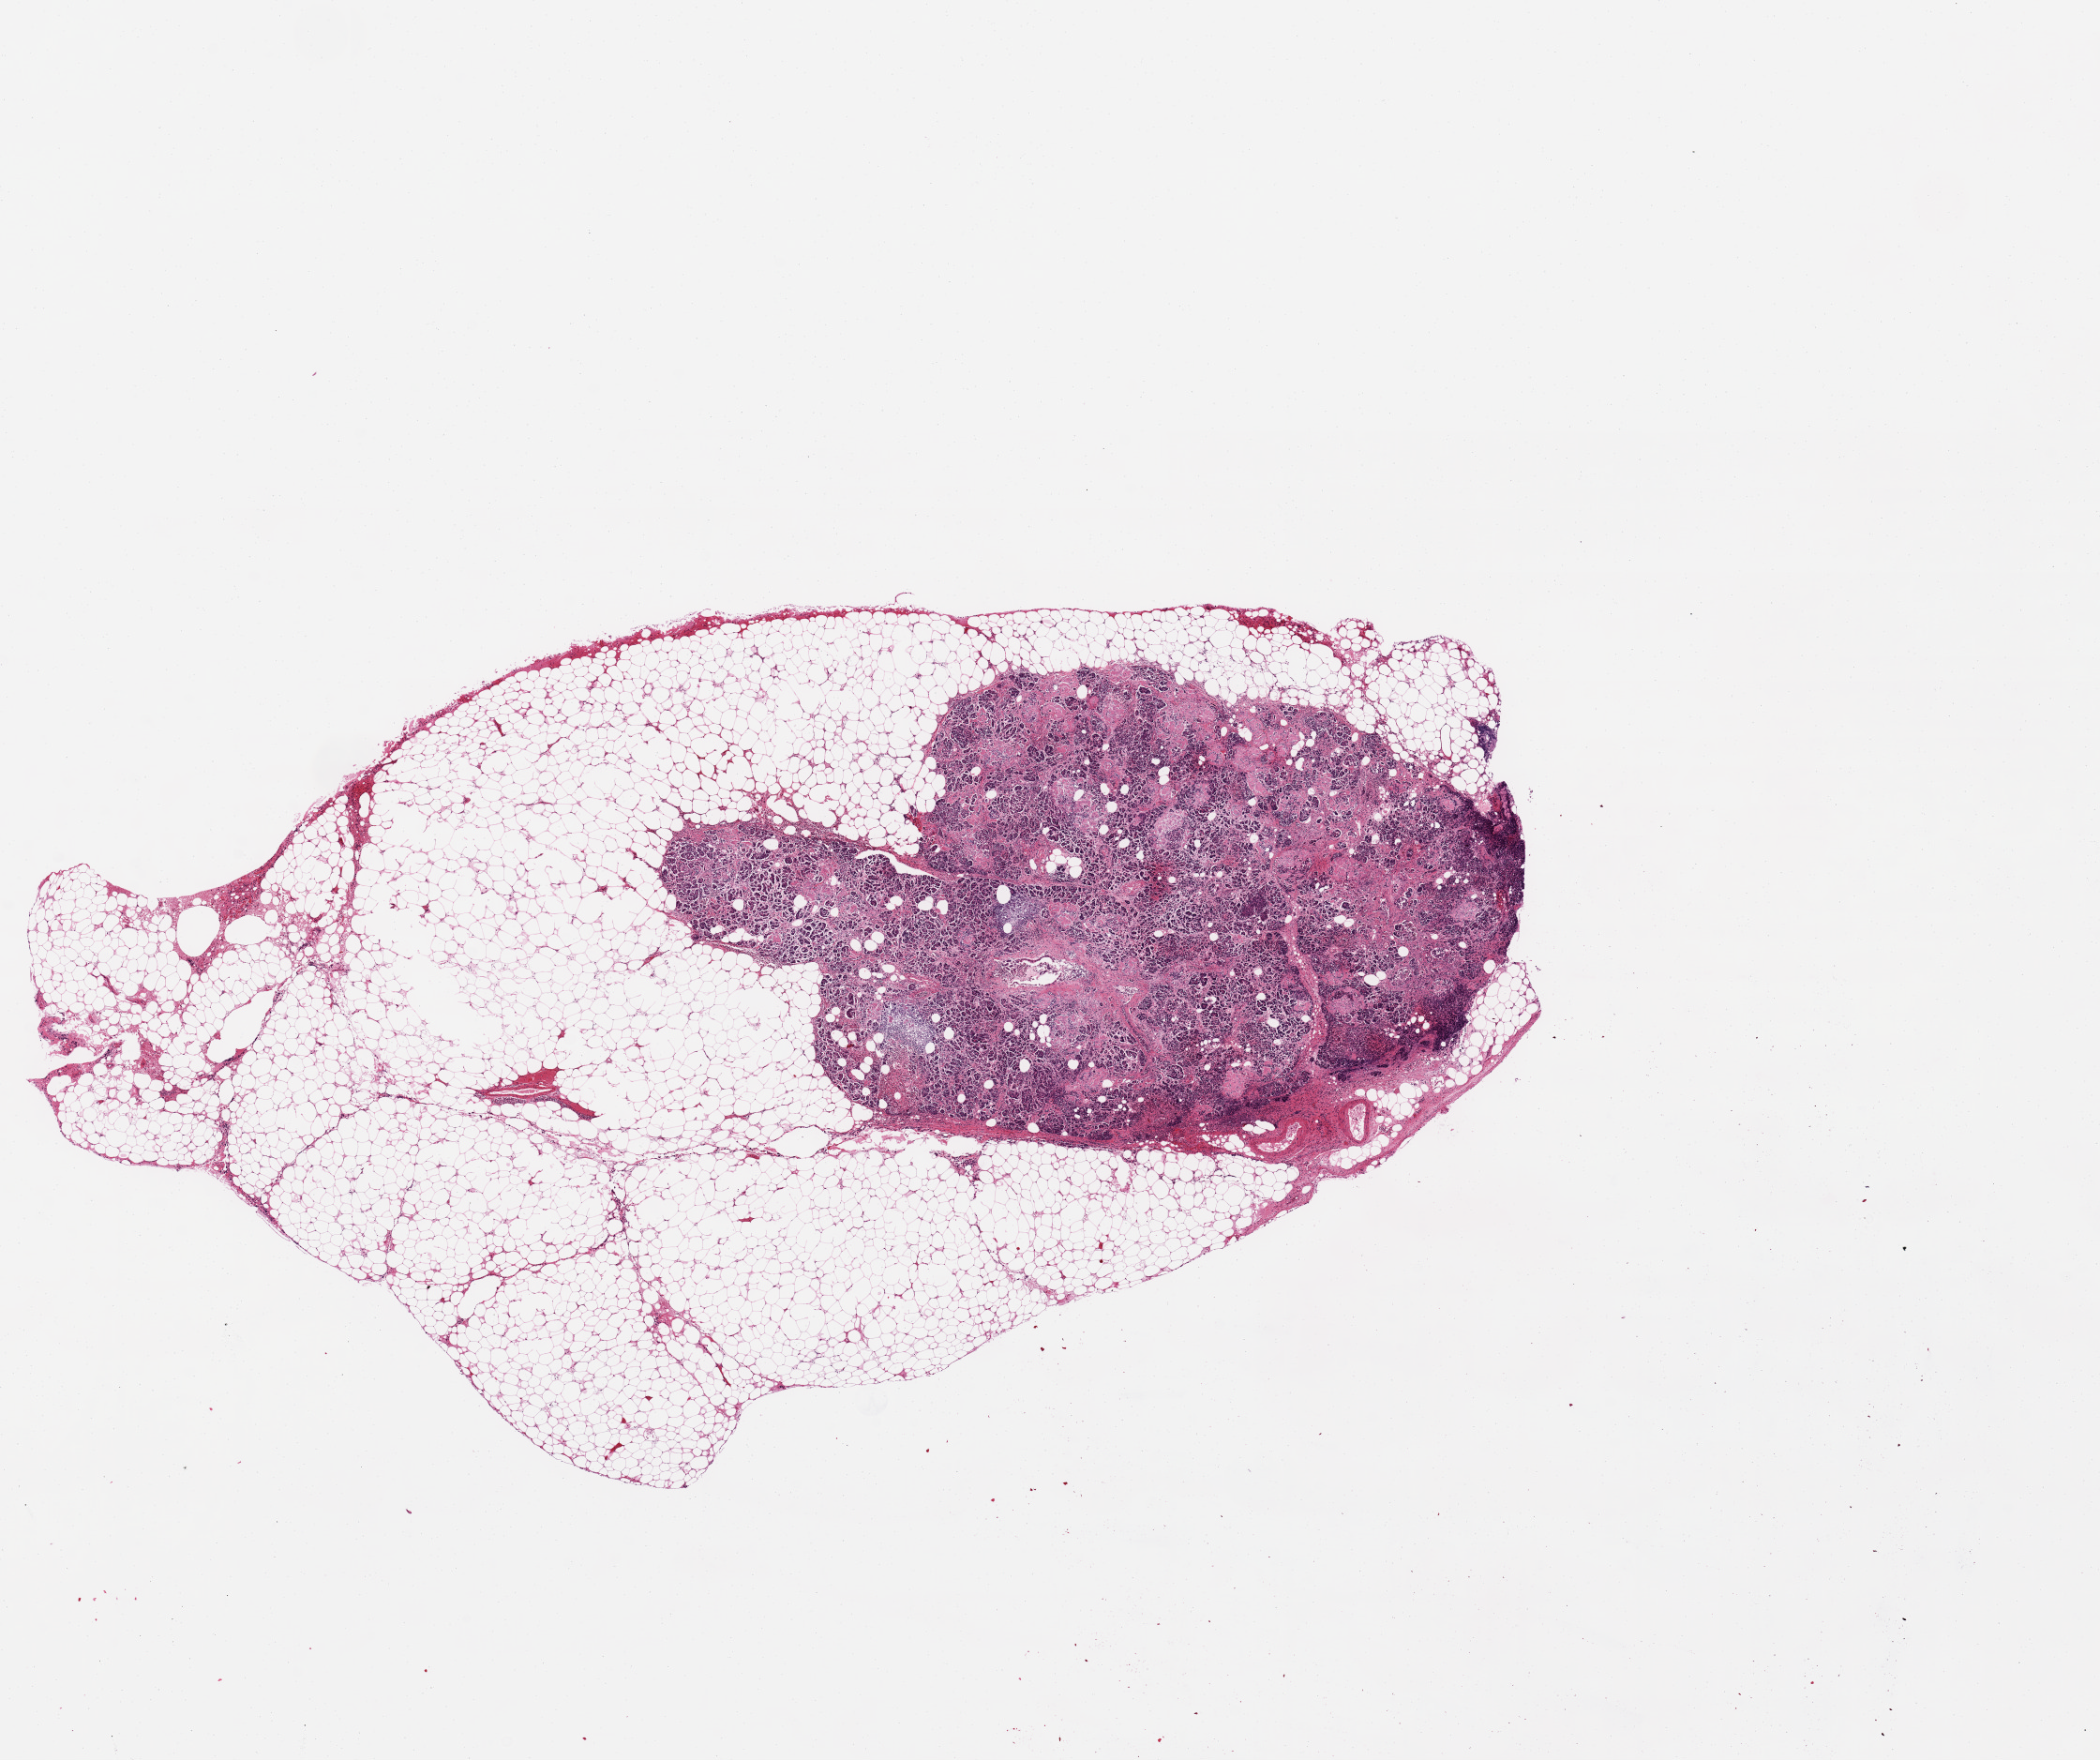
Whole-slide image, H&E stain — a low-resolution overview of the entire scanned area, about 17.7 x 14.8 mm (acquisition: 20x scan); PAXgene-fixed, paraffin-embedded tissue; sampled site (target tissue): pancreas; tissue donor sample. Donor sex: male.
* reviewer comment on this tissue sample: parenchymal hyaline sclerosis 25%; fat is 50% of aliquot